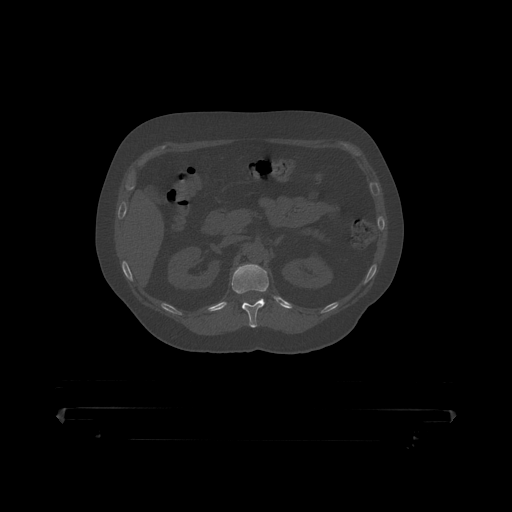
CT including the spine, one axial slice; position 164 of 390 along the scan axis; bone window (W 1800 / L 400 HU); 1.25 mm slice thickness; 512 × 512 image matrix, field of view 650 × 650 mm. Male patient, age 60 years. Case-level facts recorded for this patient, not image findings: primary cancer: prostate.
Structures marked on this image (semi-automatically segmented with operator editing):
- T12 vertebra: bounding box <232,264,269,319> (left, top, right, bottom; pixels)